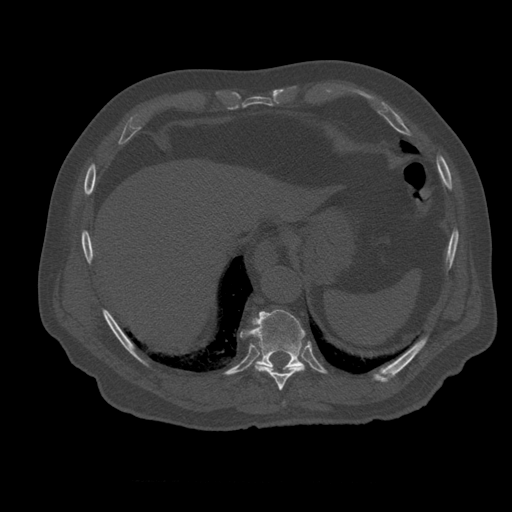
CT including the spine, one axial slice. Position 310 of 399 along the scan axis. Reconstruction kernel STANDARD. Bone window (W 1800 / L 400 HU). 1.25 mm slice thickness. 512 × 512 image matrix, field of view 407 × 407 mm. Patient age 73 years. From the clinical record (not read from this slice): primary cancer: prostate.
Structures marked on this image (semi-automatically segmented with operator editing):
- T10 vertebra: bounding box [x1, y1, x2, y2] px = [241, 310, 305, 369]
- T12 vertebra: [267, 346, 280, 359]
- T9 vertebra: [255, 362, 305, 391]